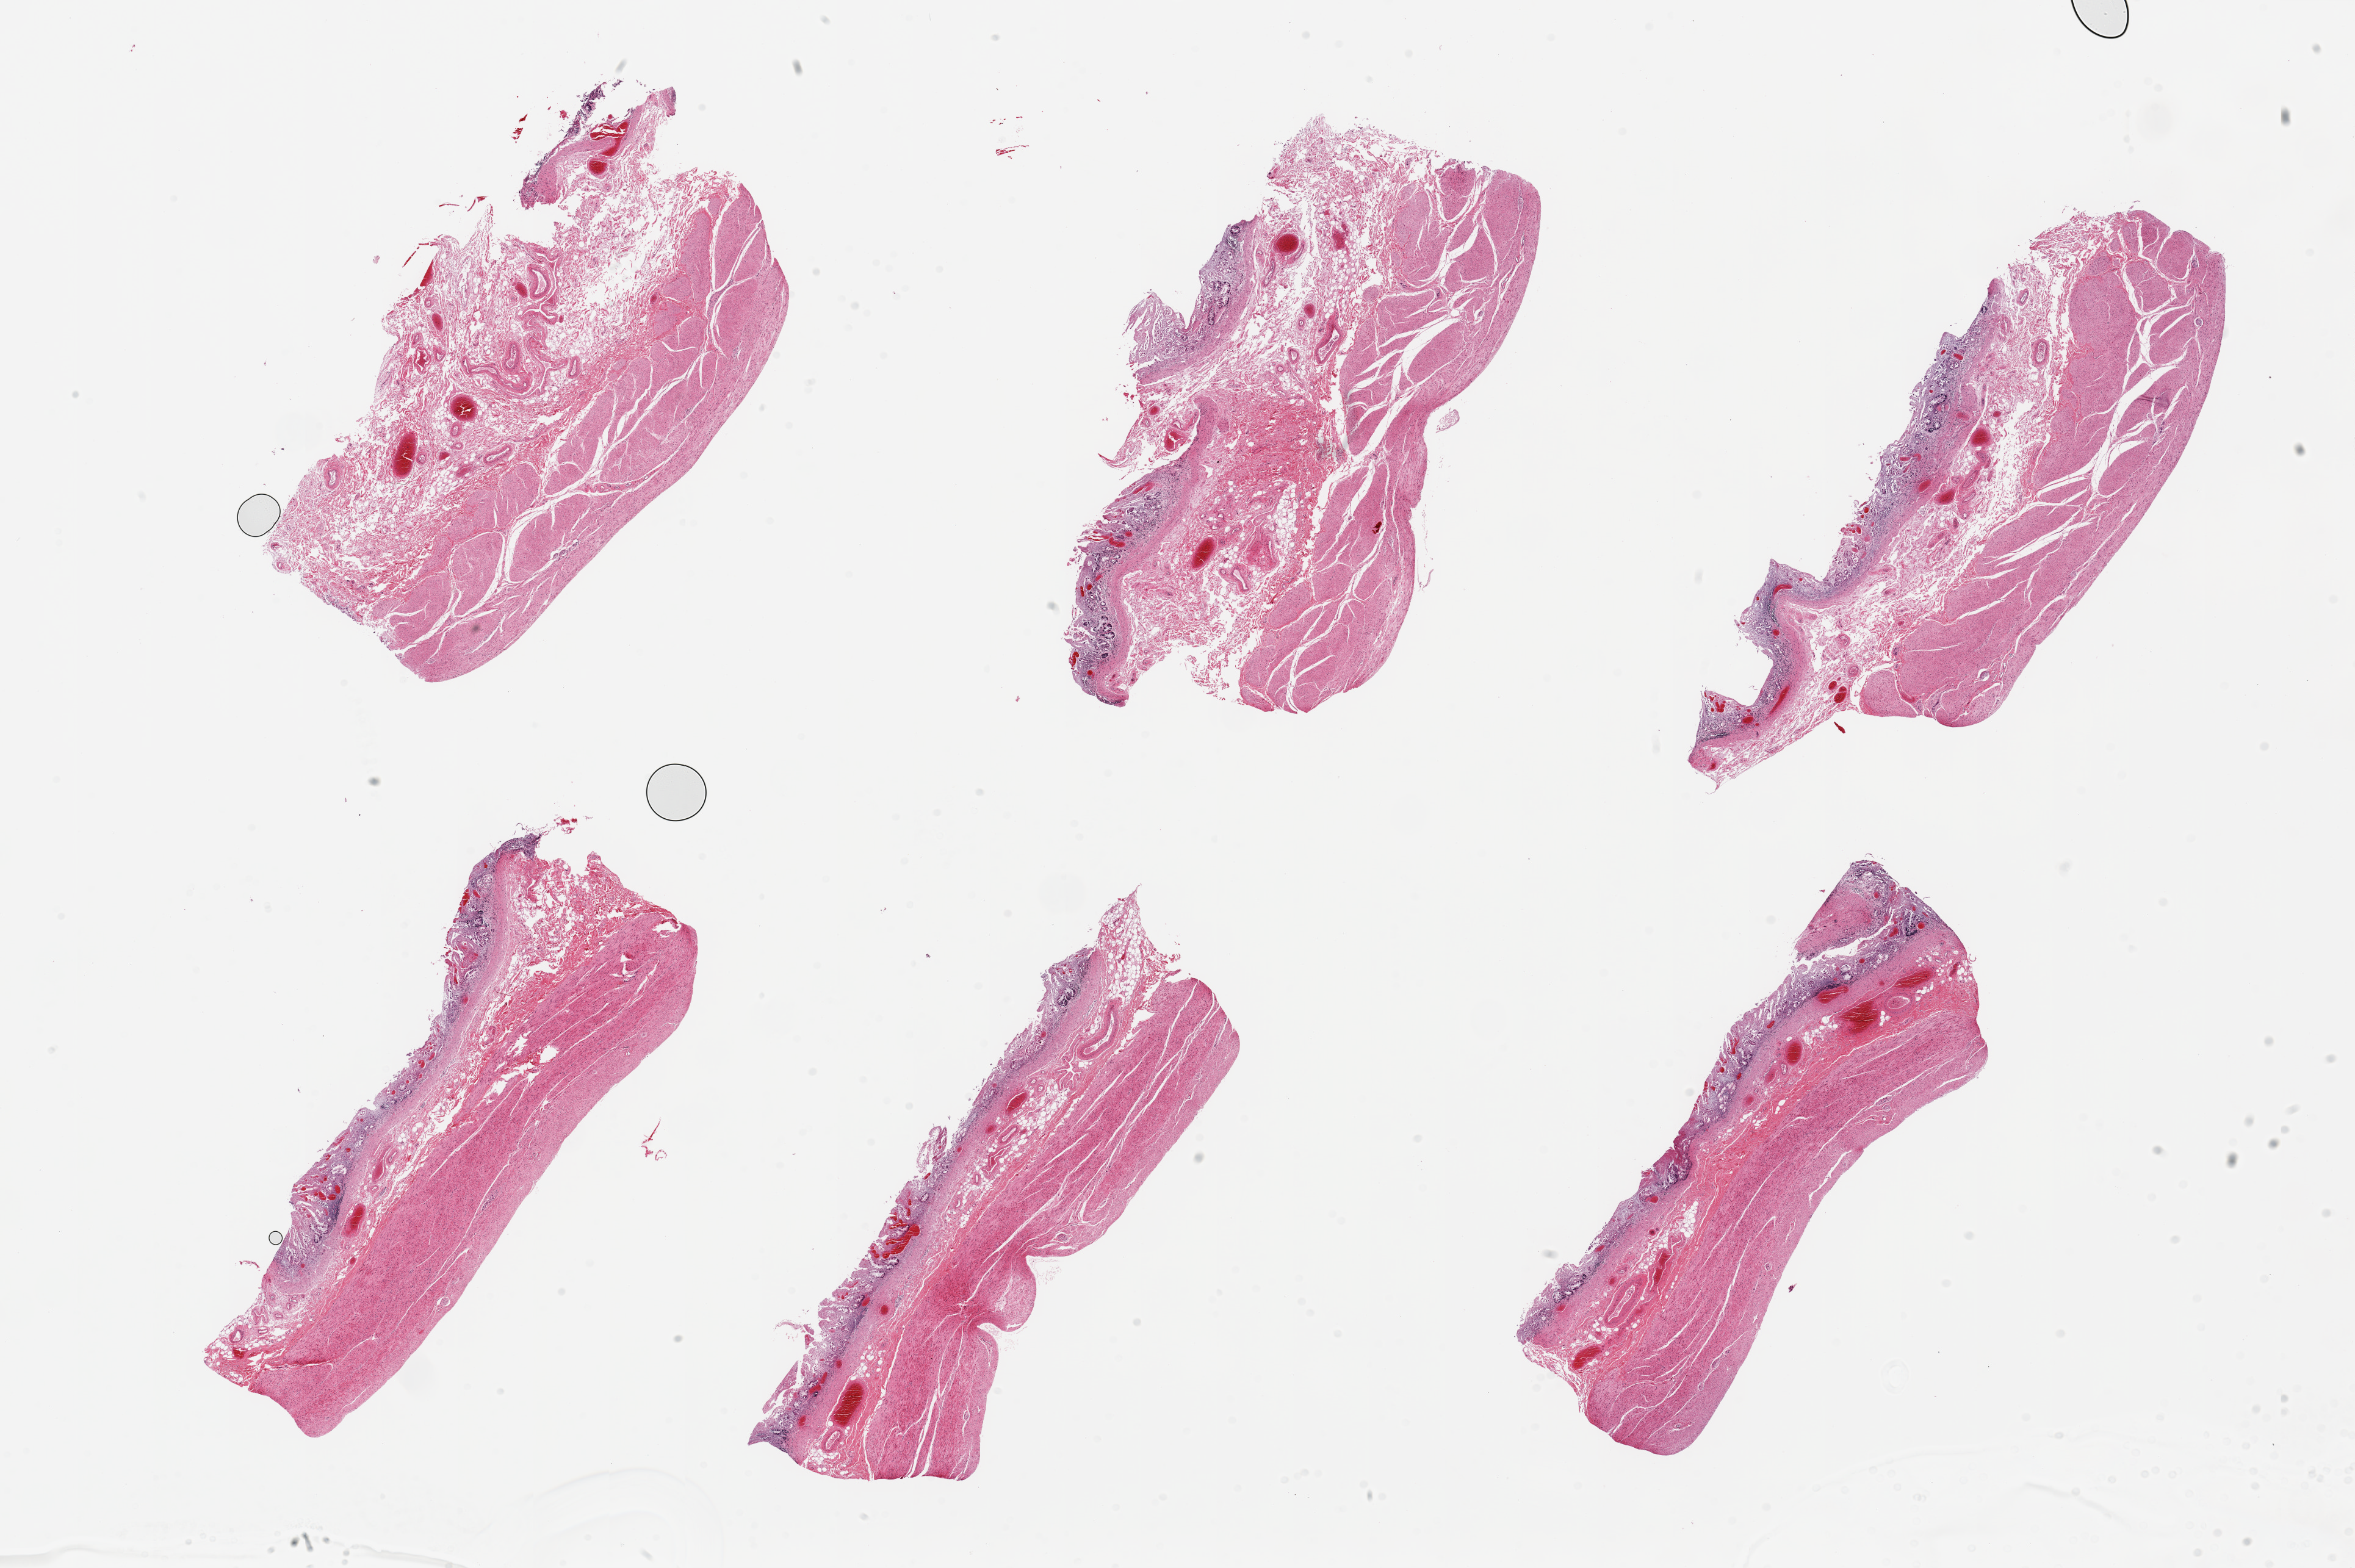
H&E whole-slide image — whole scanned area (about 30.5 x 20.3 mm) shown as a low-resolution overview. PAXgene-fixed paraffin-embedded (PFPE) section. Target tissue: stomach. Tissue donor sample.
Pathologist's review note for this sample: 6 pieces, up to 9x4mm; mucosa=3; muscularis =2.